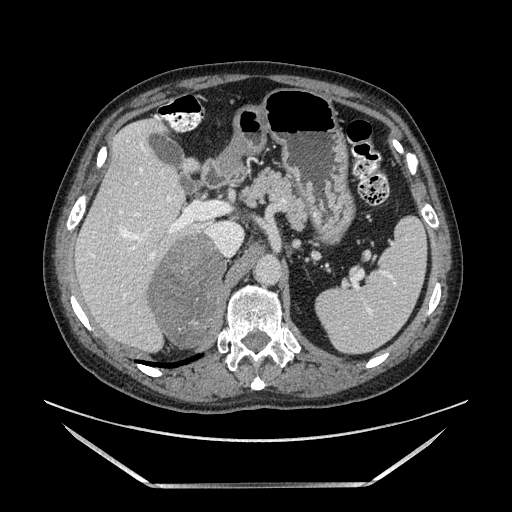
Contrast-enhanced abdominal CT, one axial slice. Position 94 of 185 along the scan axis. Soft-tissue window (W 400 / L 40 HU). 1.25 mm slice thickness. 512 × 512 image matrix. Male patient. Case-level facts recorded for this patient, not image findings: diagnosis: adrenocortical carcinoma; tumour side: right adrenal; tumour size at pathology: 10.3 cm.
Structures marked on this image (semi-automatically segmented with operator editing):
- mass: bounding box (x1, y1, x2, y2) in pixels: (152, 232, 226, 345)